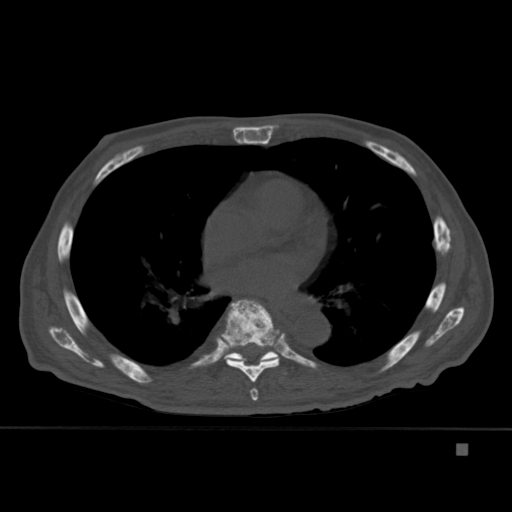
CT including the spine, one axial slice; position 275 of 451 along the scan axis; bone window (W 1800 / L 400 HU); 512 × 512 image matrix. Patient: male, 75 years. From the clinical record (not read from this slice): primary cancer: prostate.
Structures marked on this image (semi-automatic segmentation, software-assisted and operator-edited):
- T6 vertebra: bounding box (x1, y1, x2, y2) in pixels: (250, 388, 258, 401)
- T7 vertebra: (221, 299, 282, 383)
- T8 vertebra: (224, 303, 287, 374)